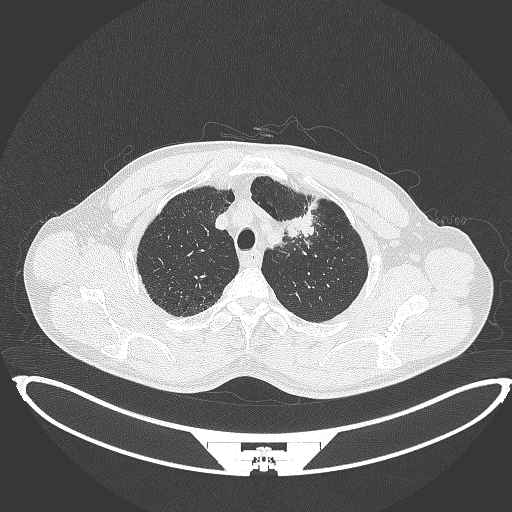
Chest CT, one axial slice; position 366 of 395 along the scan axis; 120 kVp; lung window (W 1500 / L -600 HU); 1 mm slice thickness; 512 × 512 image matrix, field of view 457 × 457 mm. Patient: male, 60 years. Case-level facts recorded for this patient, not image findings: clinical TNM (as recorded): T2a N0 M0.
Annotated regions visible in this slice (bounding box drawn by a radiologist):
- lung tumour (recorded histology: squamous cell carcinoma): bounding box <283,207,318,242> (left, top, right, bottom; pixels)